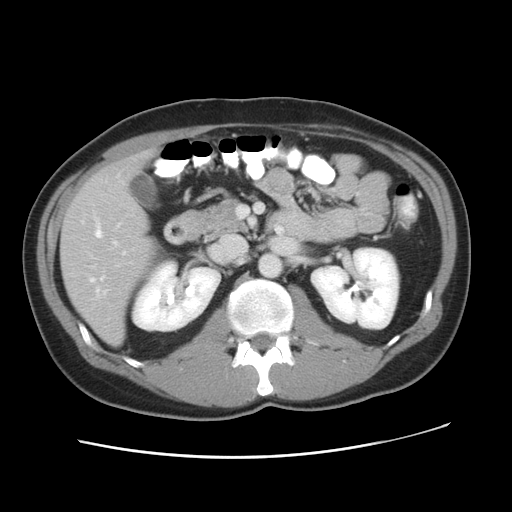
Contrast-enhanced abdominal CT, one axial slice. Slice 23 of 49 in the series (ordered by position). Reconstruction kernel STANDARD. 120 kVp. Intravenous contrast given. Soft-tissue window (W 400 / L 40 HU). 5 mm slice thickness. 512 × 512 image matrix, field of view 363 × 363 mm. Male patient, age 41 years. From the clinical record (not read from this slice): diagnosis: colorectal cancer liver metastases, imaged before liver resection.
Annotated regions visible in this slice (outlined manually by an expert reader):
- hepatic veins: bounding box (x1, y1, x2, y2) in pixels: (90, 222, 124, 292)
- liver: (62, 152, 151, 344)
- planned liver remnant (the part of the liver to remain after resection): (113, 151, 151, 180)
- portal vein (with intrahepatic branches): (100, 223, 120, 293)
- liver metastasis: (101, 184, 111, 194)